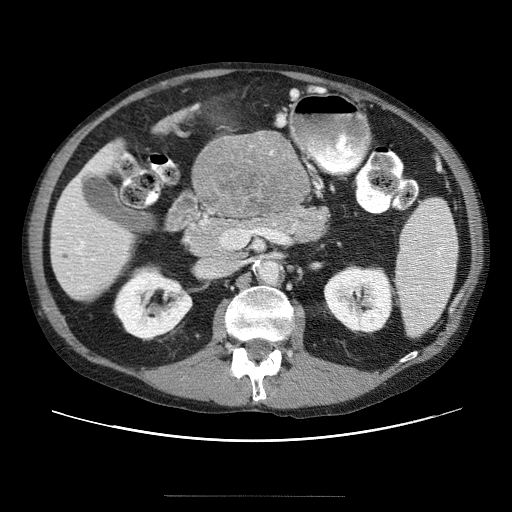
Contrast-enhanced abdominal CT (liver protocol), one axial slice. Slice 11 of 69 in the series (ordered by position). 120 kVp. Soft-tissue window (W 400 / L 40 HU). 2.5 mm slice thickness. 512 × 512 image matrix. From the clinical record (not read from this slice): diagnosis: hepatocellular carcinoma (patient treated with transarterial chemoembolisation; whether this scan precedes or follows treatment is not stated here); TNM stage (as recorded): Stage-IVB; Child-Pugh class: B; tumour differentiation: poorly differentiated; tumour nodularity: multinodular.
Annotated regions visible in this slice (semi-automatically segmented with operator editing):
- liver parenchyma outside the tumour (the mass and vessels are separate outlines, so this box may not span the whole liver): bounding box [x1, y1, x2, y2] px = [50, 136, 313, 296]
- mass: [192, 134, 310, 223]
- liver vessels: [65, 220, 116, 292]